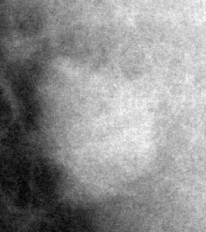
Region of interest cut from a scanned film mammogram (one marked finding); right breast; MLO view.
- Marked abnormality: mass, shape round, margins circumscribed; BI-RADS assessment category 4; subtlety rating 5 on a 1 (subtle) to 5 (obvious) scale; pathology result (as recorded, not read from the image): malignant.